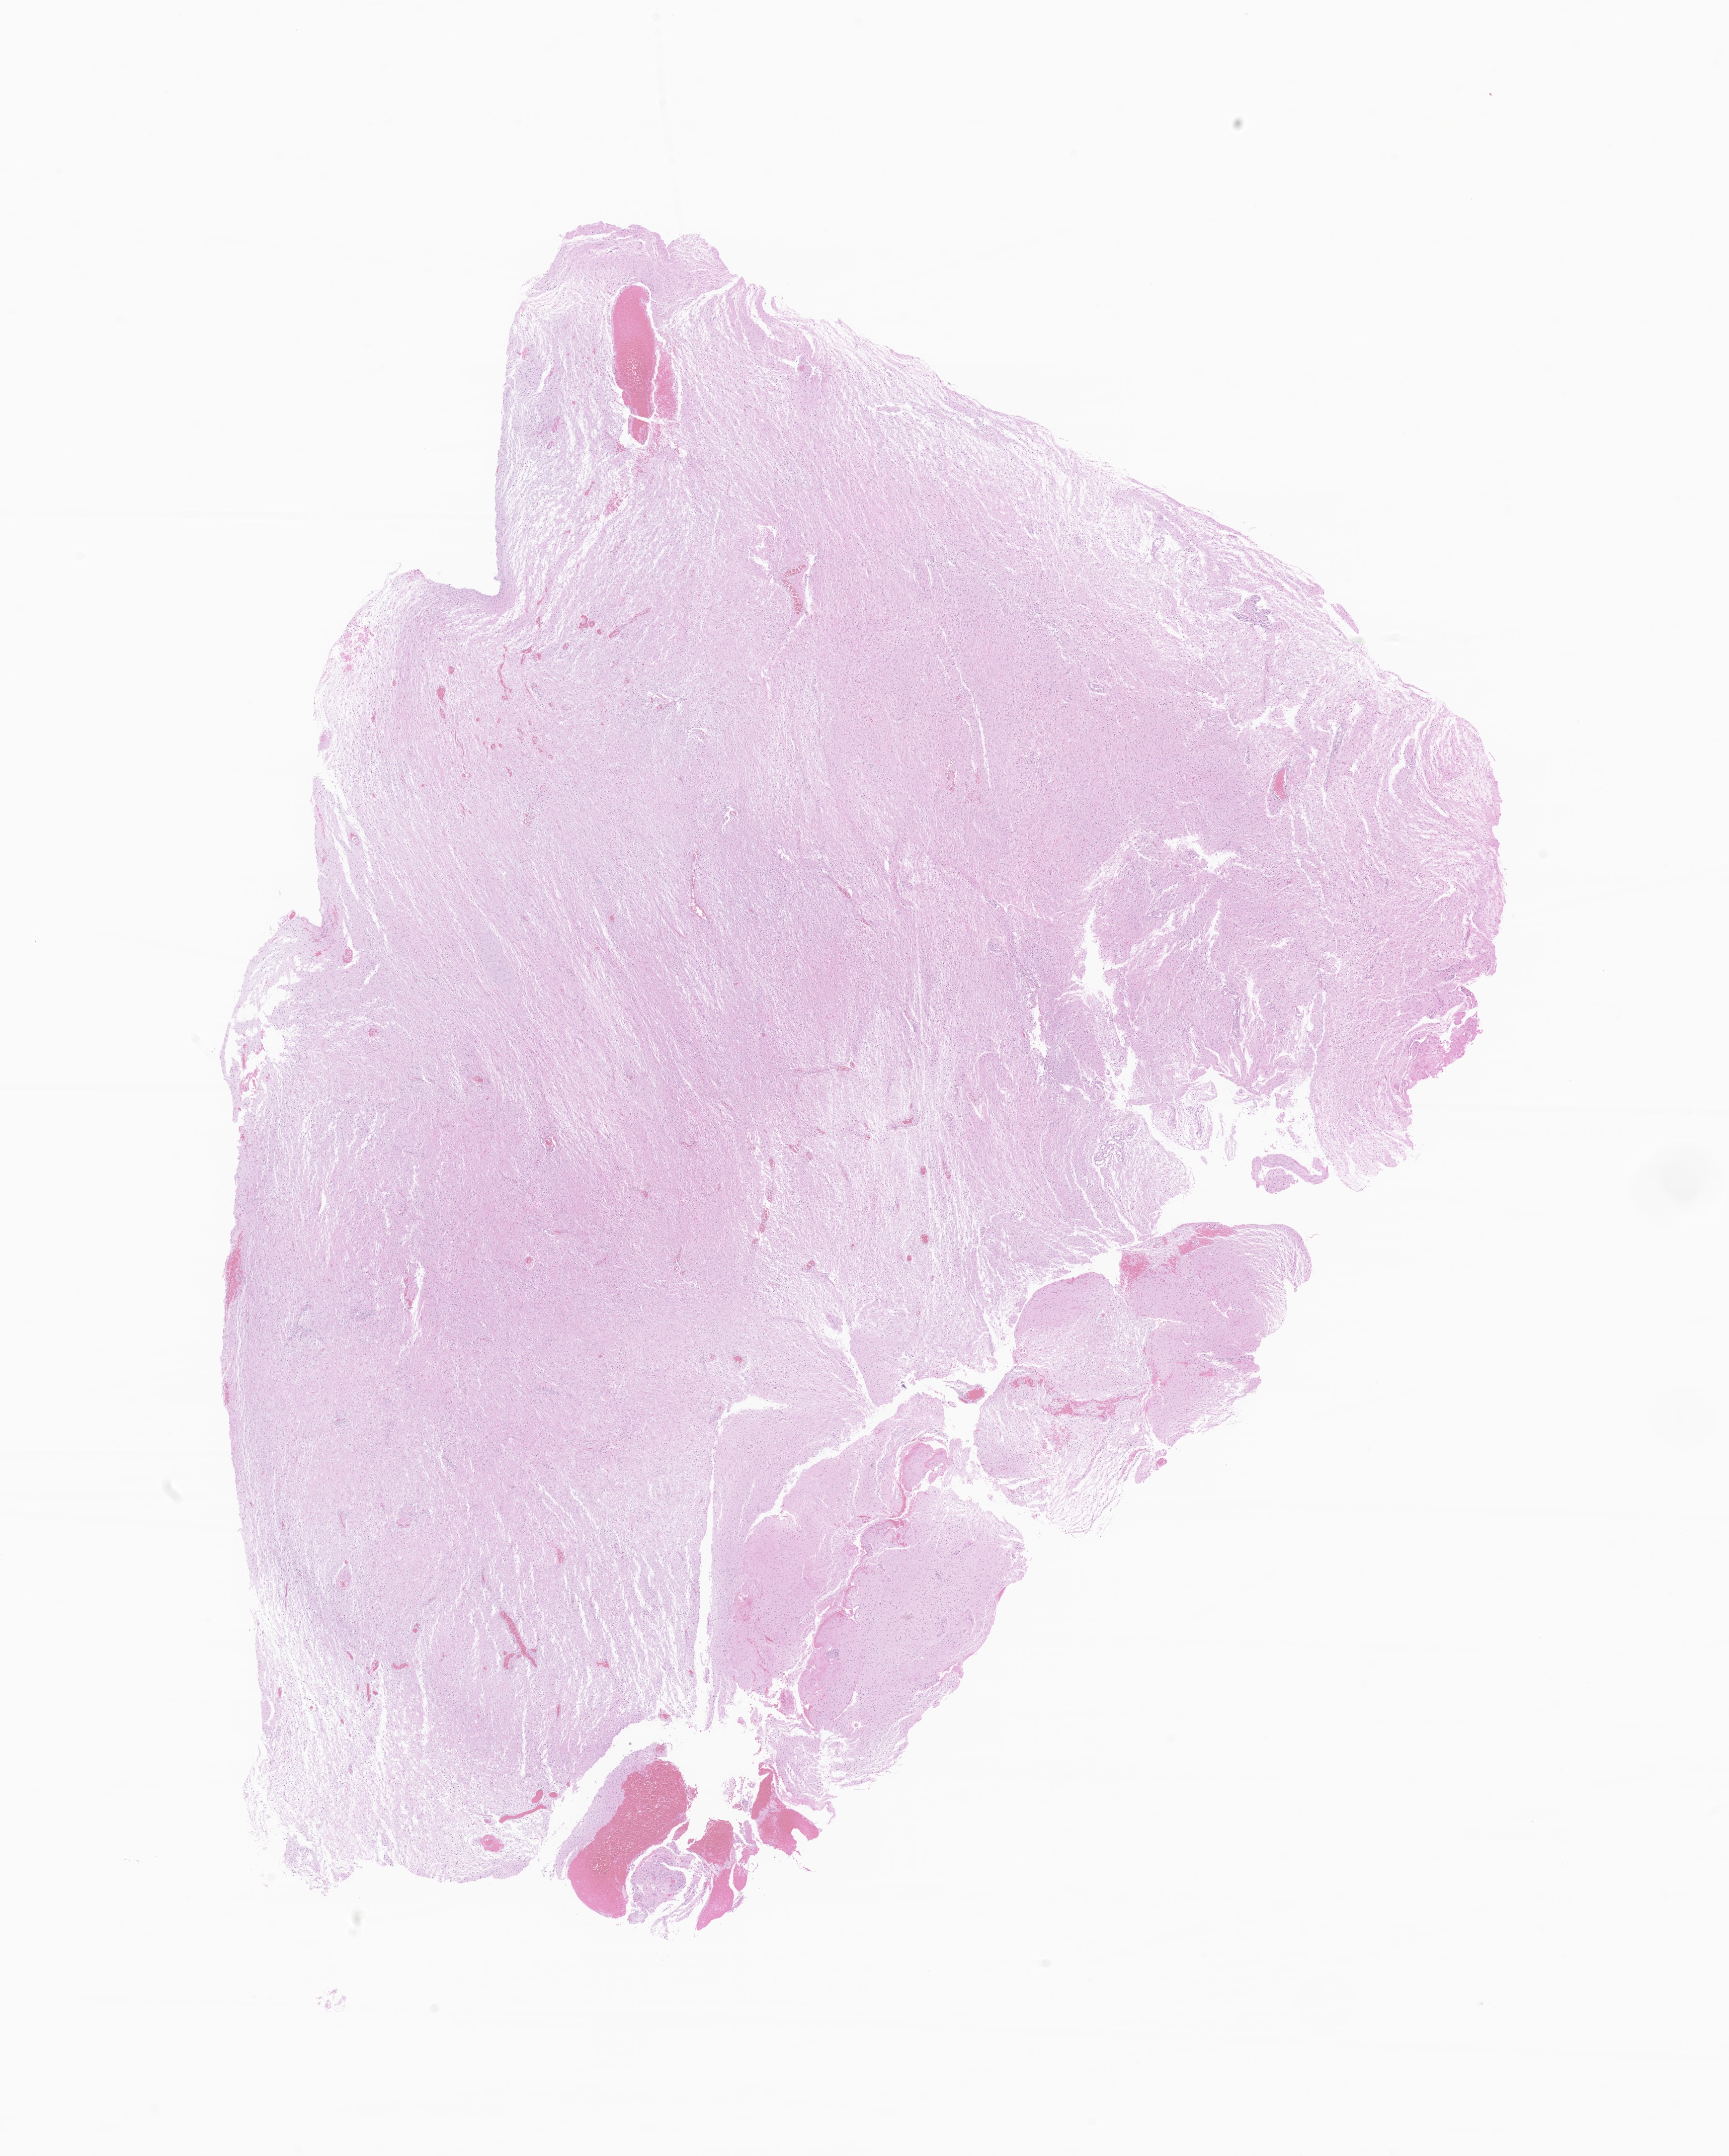
Whole-slide image, hematoxylin and eosin (H&E) stain of tumor tissue from the brain, shown as a low-resolution overview of the whole scanned area (about 14.5 x 18.1 mm), FFPE section. Male patient, age 92 months.
Diagnosis: Pilocytic astrocytoma.